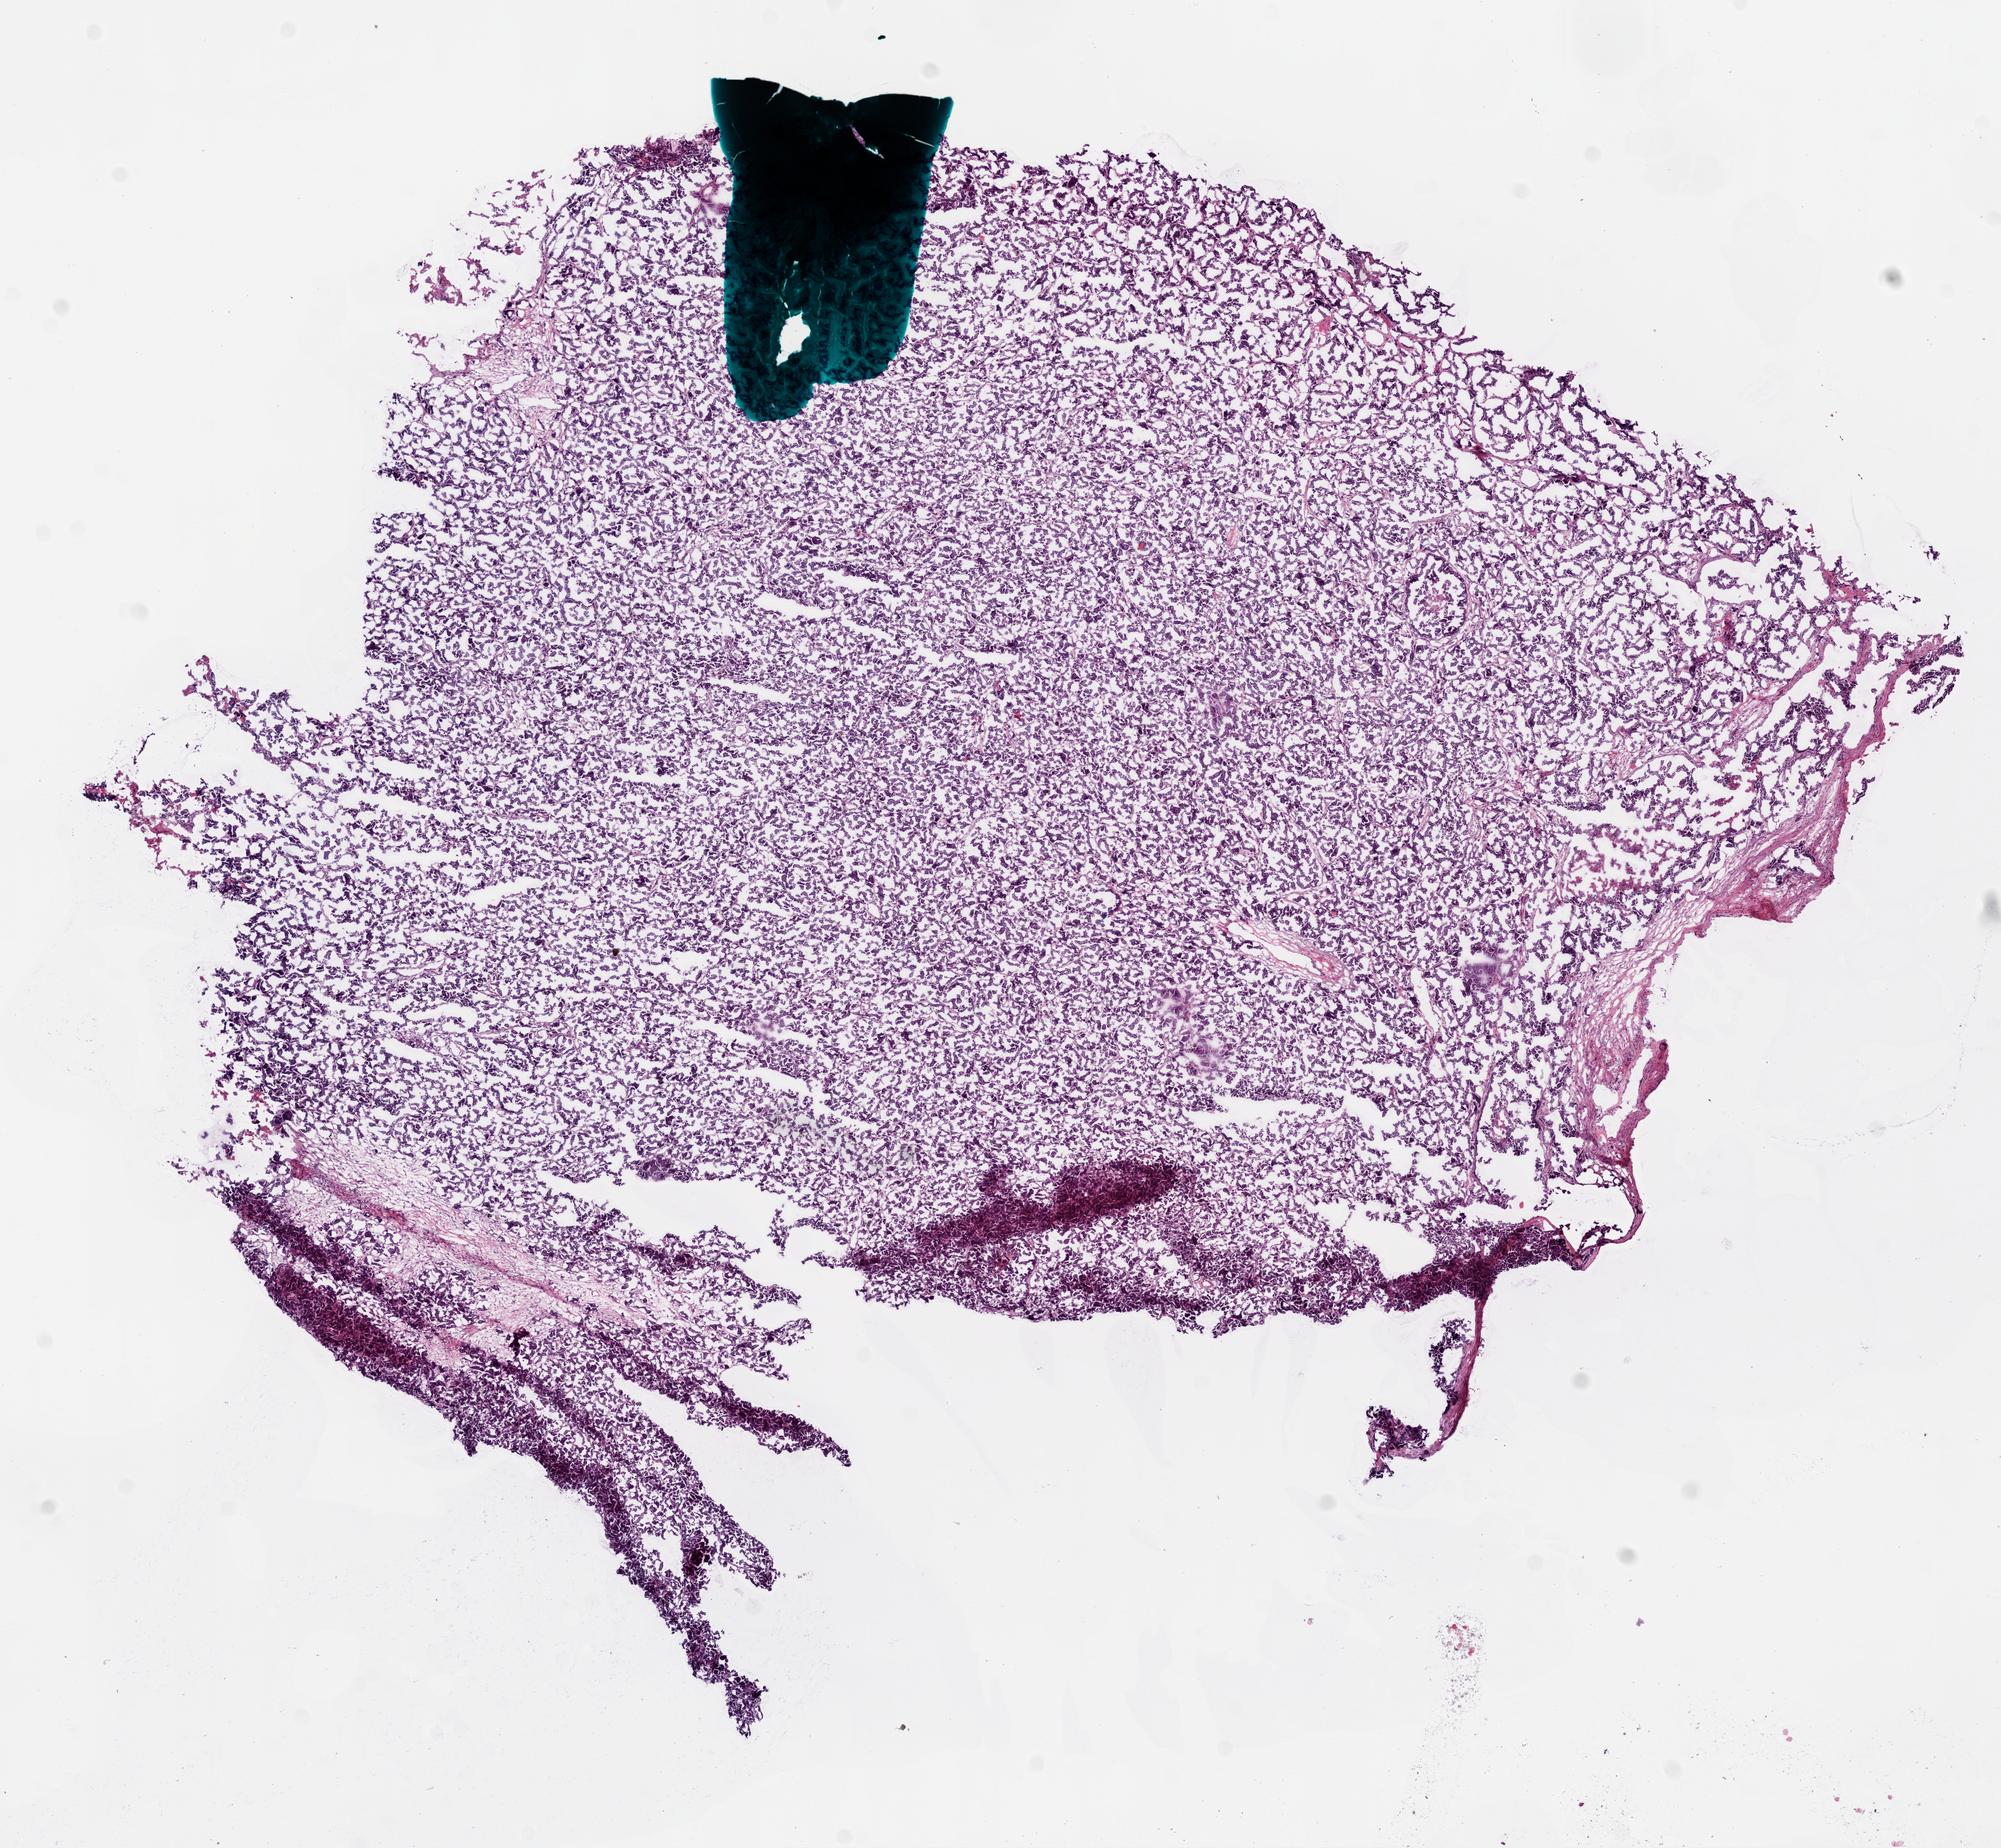
H&E-stained whole-slide image, a low-resolution overview of the entire scanned area, about 11.1 x 10.3 mm; frozen section from the bottom of the tissue portion; ovary, primary tumour sample. Patient: female, age at initial diagnosis 48 years. Histologic grade: G3 (poorly differentiated). Pathologist review of this section (percent, as recorded): tumour nuclei 95%, normal cells 0%, necrosis 1%.
FIGO stage: IV. Diagnosis: Serous cystadenocarcinoma, NOS. Laterality: left.